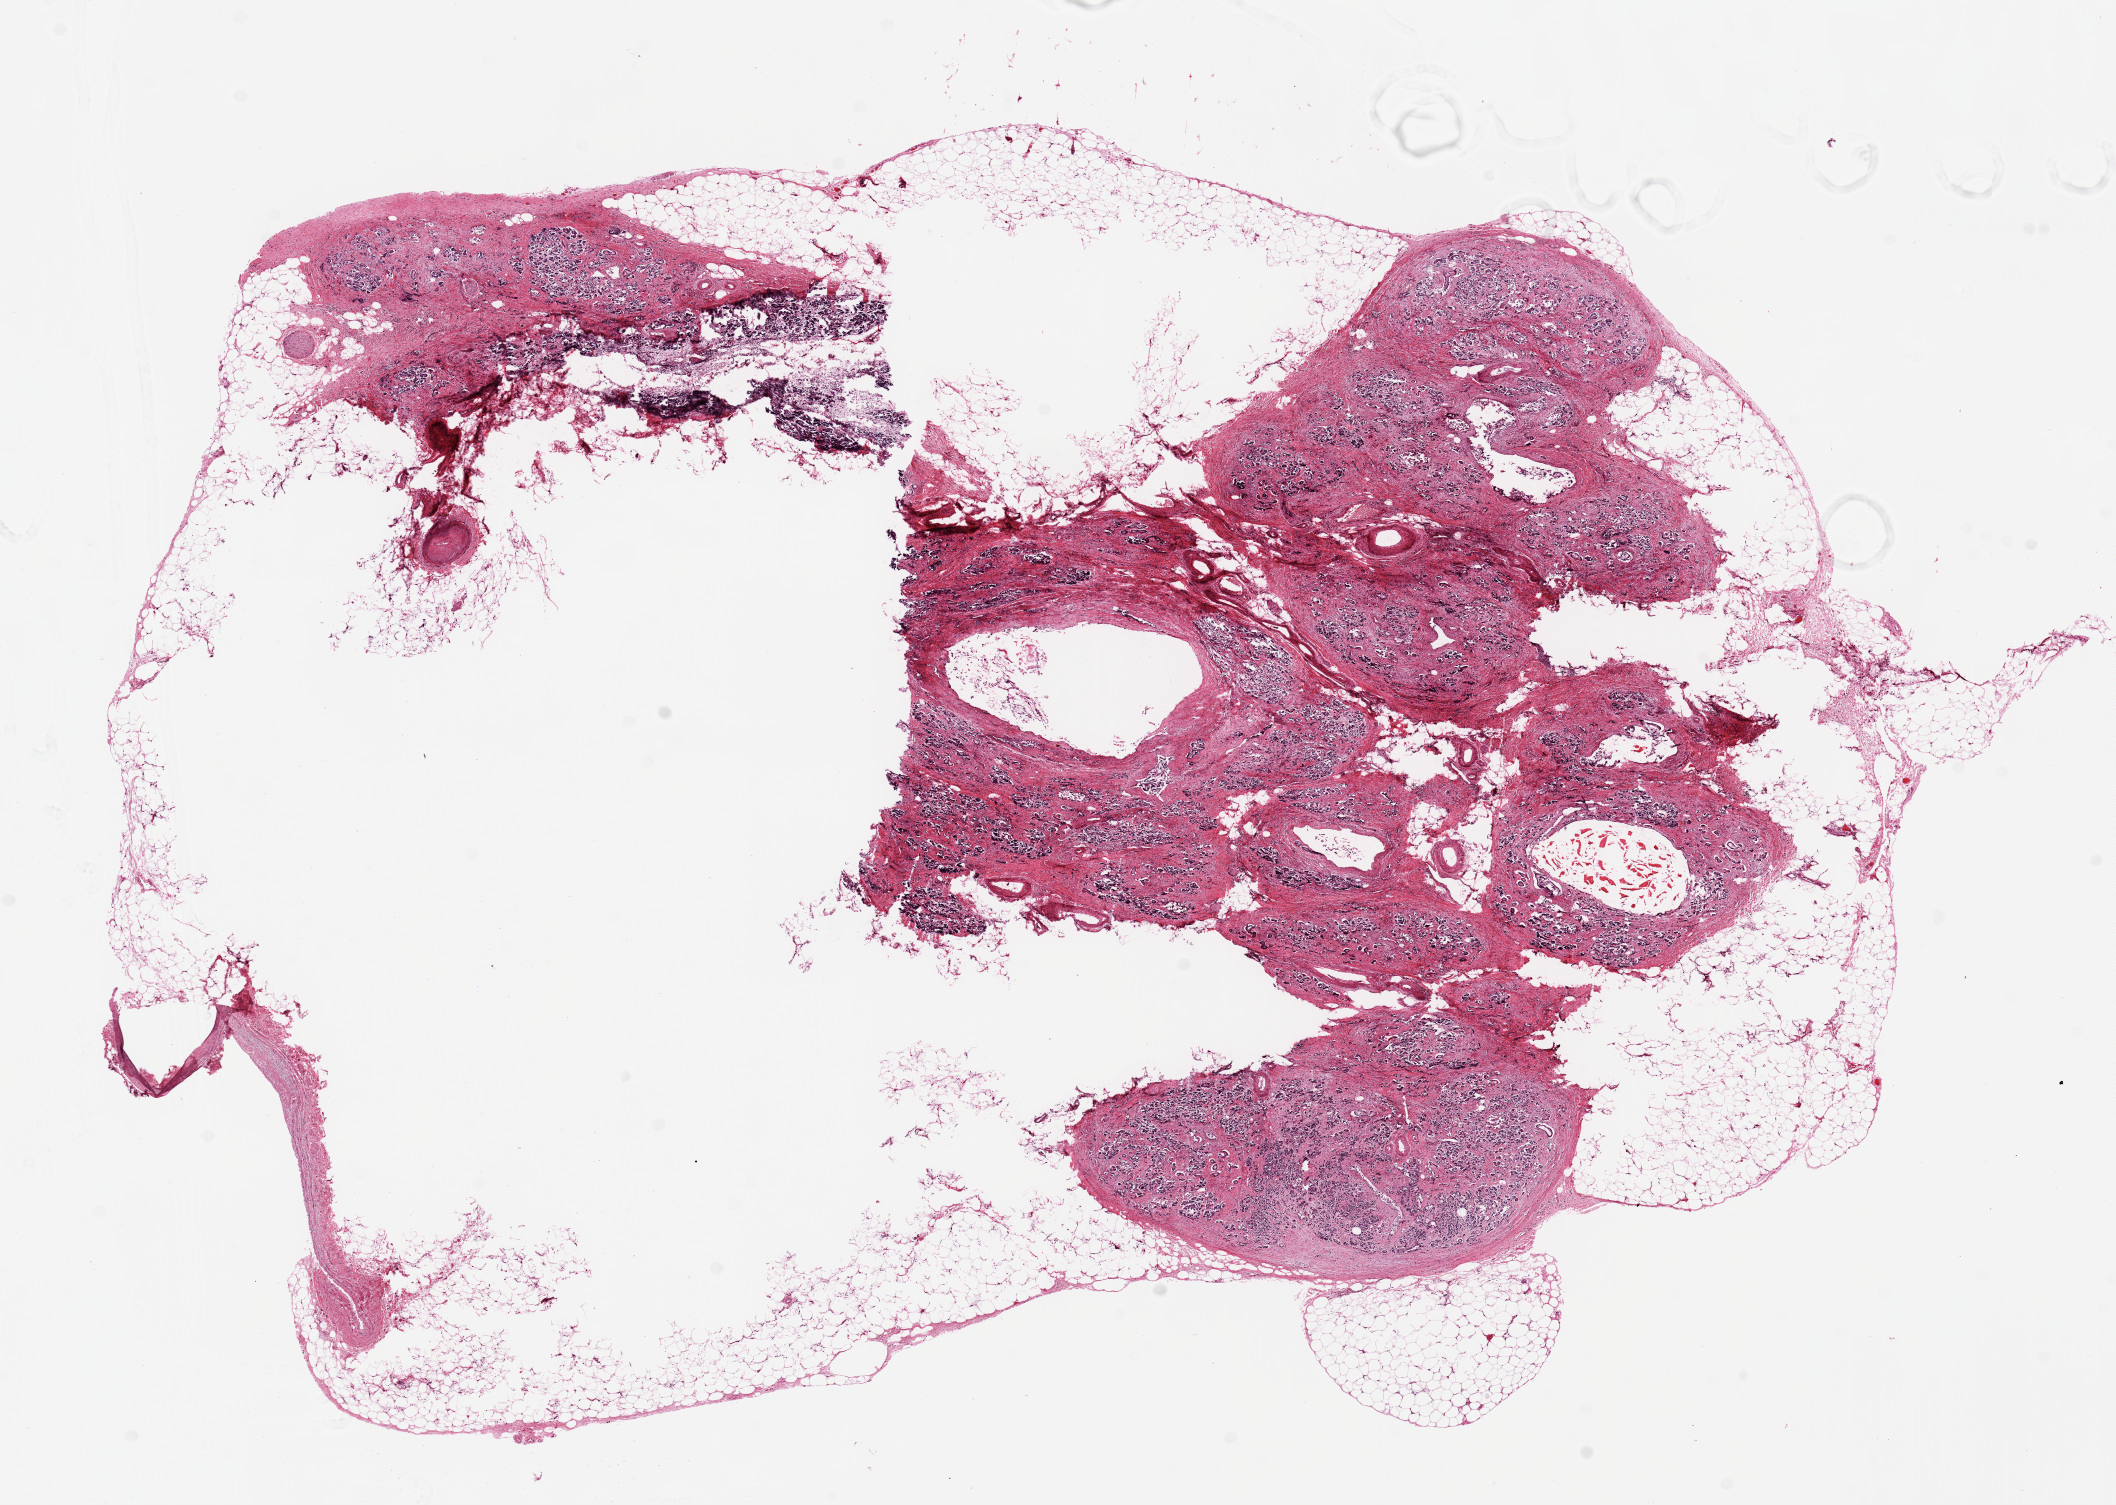
Digitized haematoxylin and eosin-stained section — whole scanned area (about 16.7 x 11.9 mm, from a 20x scan) shown as a low-resolution overview; PAXgene-fixed paraffin-embedded (PFPE) section; section of pancreas (target tissue); donor tissue sample. Donor: female.
- pathologist's review note for this sample: Severe autolysis (???3???) and very fibrotic. Parenchyma ~40-50% of specimen